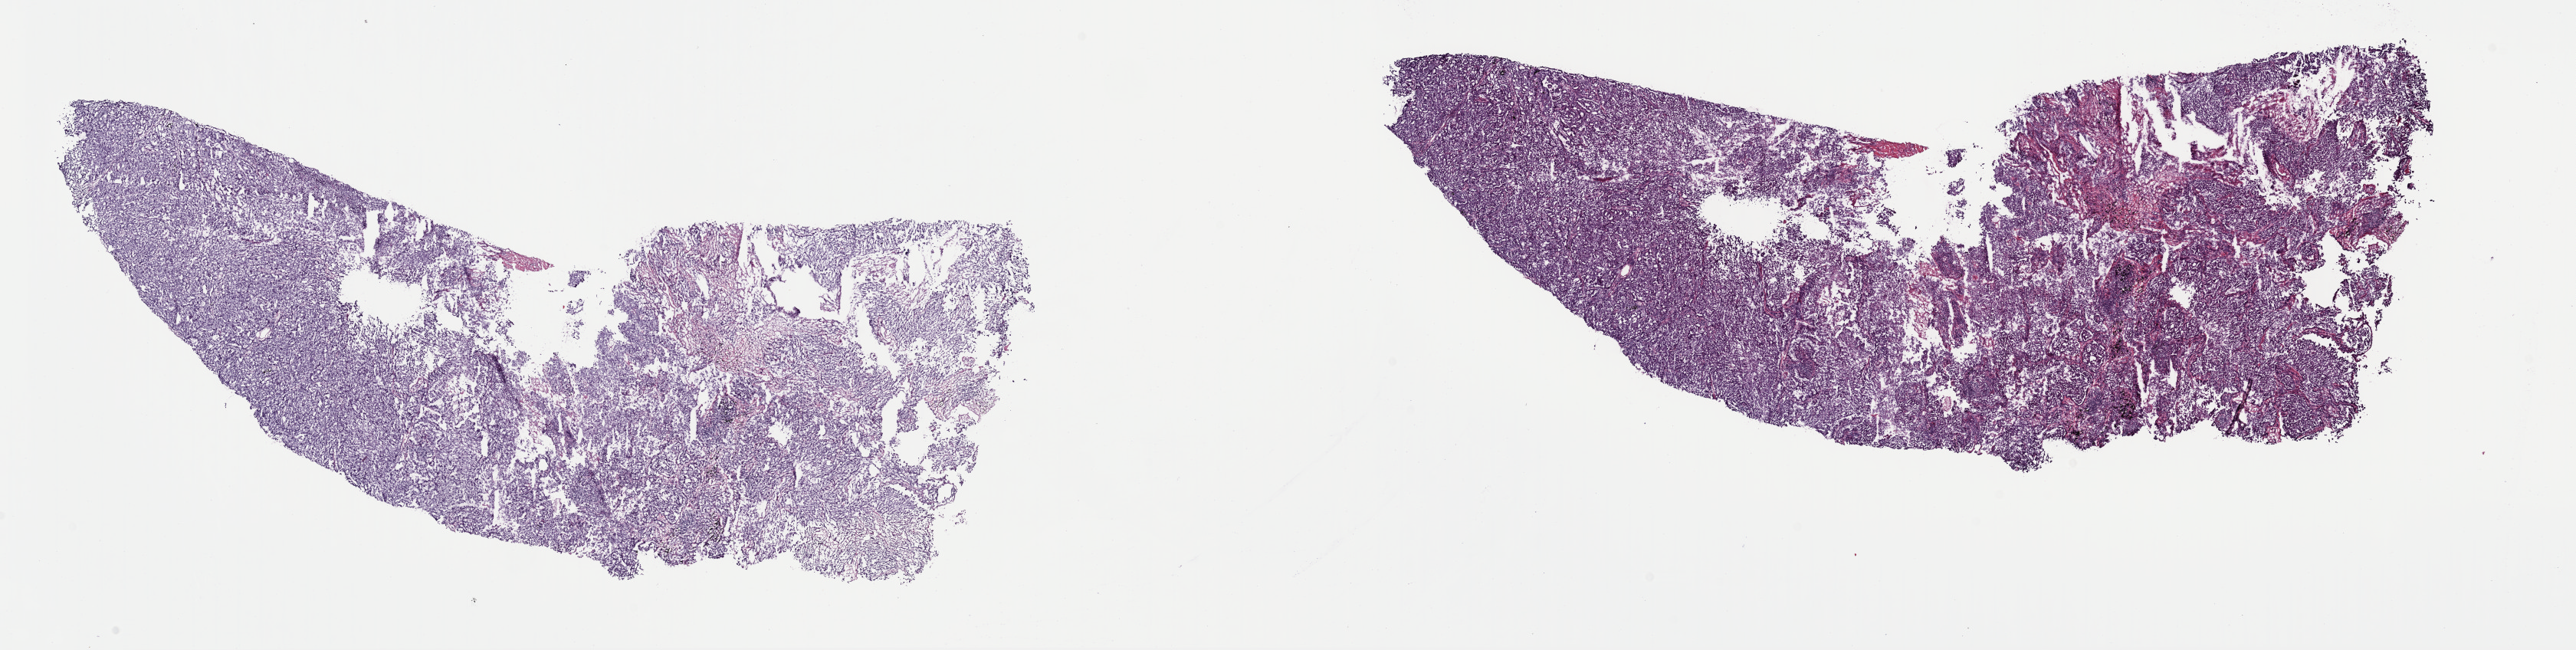
Whole-slide histology image, H&E — low-resolution overview of the scanned area, about 26.5 x 6.7 mm, frozen section from the top of the tissue portion, primary tumour sample from the lung. Male patient; age at initial diagnosis 71 years. Pathologist review of this section (percent, as recorded): tumour cells 100%, tumour nuclei 88%, normal cells 0%, stromal cells 0%, necrosis 0%. Inflammatory infiltration, as recorded: lymphocyte infiltration 0%, monocyte infiltration 0%, neutrophil infiltration 0%.
• diagnosis: Adenocarcinoma, NOS (lower lobe, lung)
• AJCC pathologic stage: IA (6th edition)